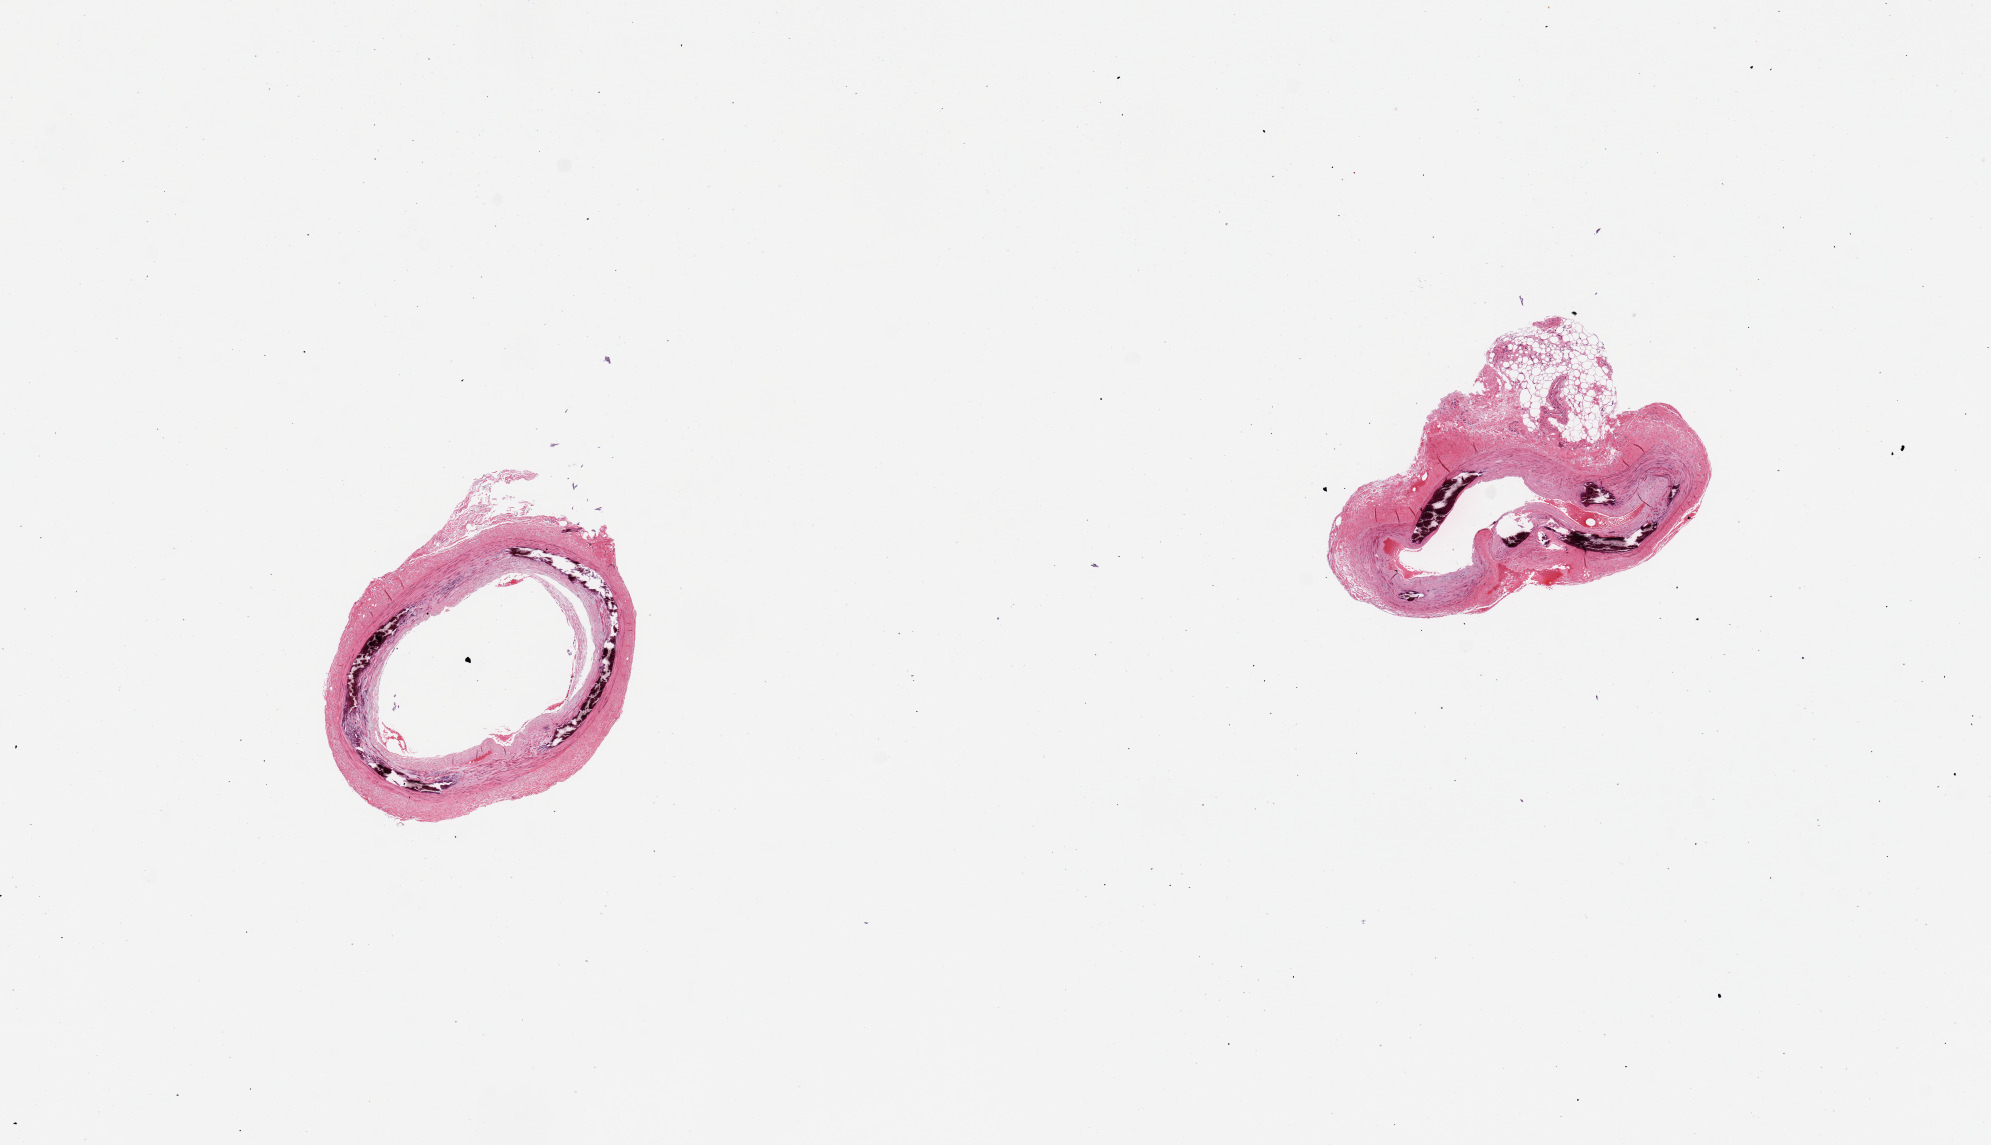
Digitized haematoxylin and eosin-stained section — low-resolution overview of the scanned area, about 15.8 x 9.1 mm. PAXgene-fixed, paraffin-embedded tissue. Section of tibial artery (target tissue). Donor tissue sample. Female donor.
Reviewer comment on this tissue sample: 2 pieces; extensive [25%] medial calcification.